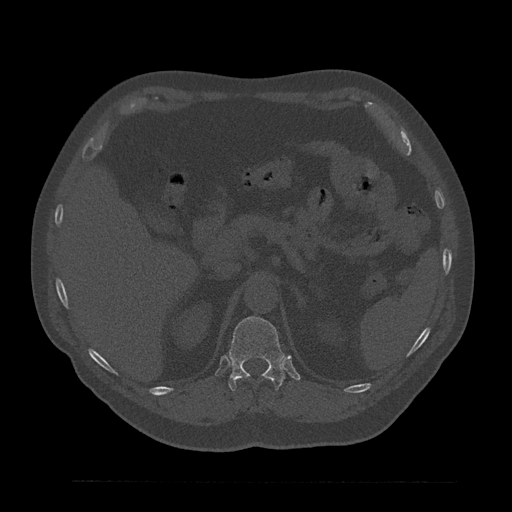
CT including the spine, one axial slice; slice 245 of 797 in the series (ordered by position); reconstruction kernel Br40s/3; 120 kVp; bone window (W 1800 / L 400 HU); 0.5 mm slice thickness; 512 × 512 image matrix, field of view 430 × 430 mm. Patient: male, 61 years. From the clinical record (not read from this slice): primary cancer: prostate.
Structures marked on this image (semi-automatic segmentation, software-assisted and operator-edited):
- T12 vertebra: box from (x=228, y=316) to (x=285, y=391) px